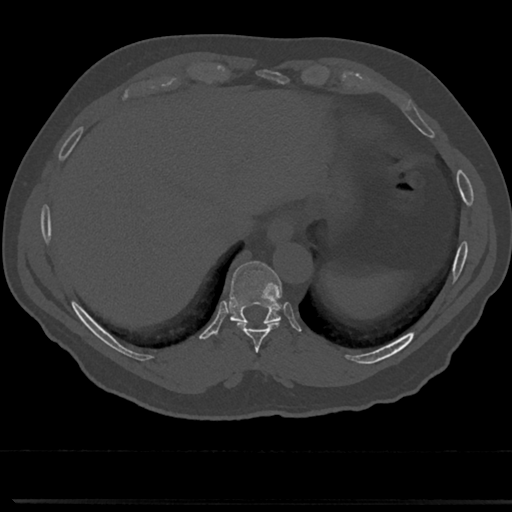
CT including the spine, one axial slice. Slice 282 of 817 in the series (ordered by position). Reconstruction kernel Br40s/3. 120 kVp. Bone window (W 1800 / L 400 HU). 512 × 512 image matrix, field of view 355 × 355 mm. Male patient, age 61 years. From the clinical record (not read from this slice): primary cancer: prostate.
Annotated regions visible in this slice (semi-automatic segmentation, software-assisted and operator-edited):
- T8 vertebra: bounding box (x1, y1, x2, y2) in pixels: (254, 354, 264, 372)
- T9 vertebra: (212, 262, 303, 350)